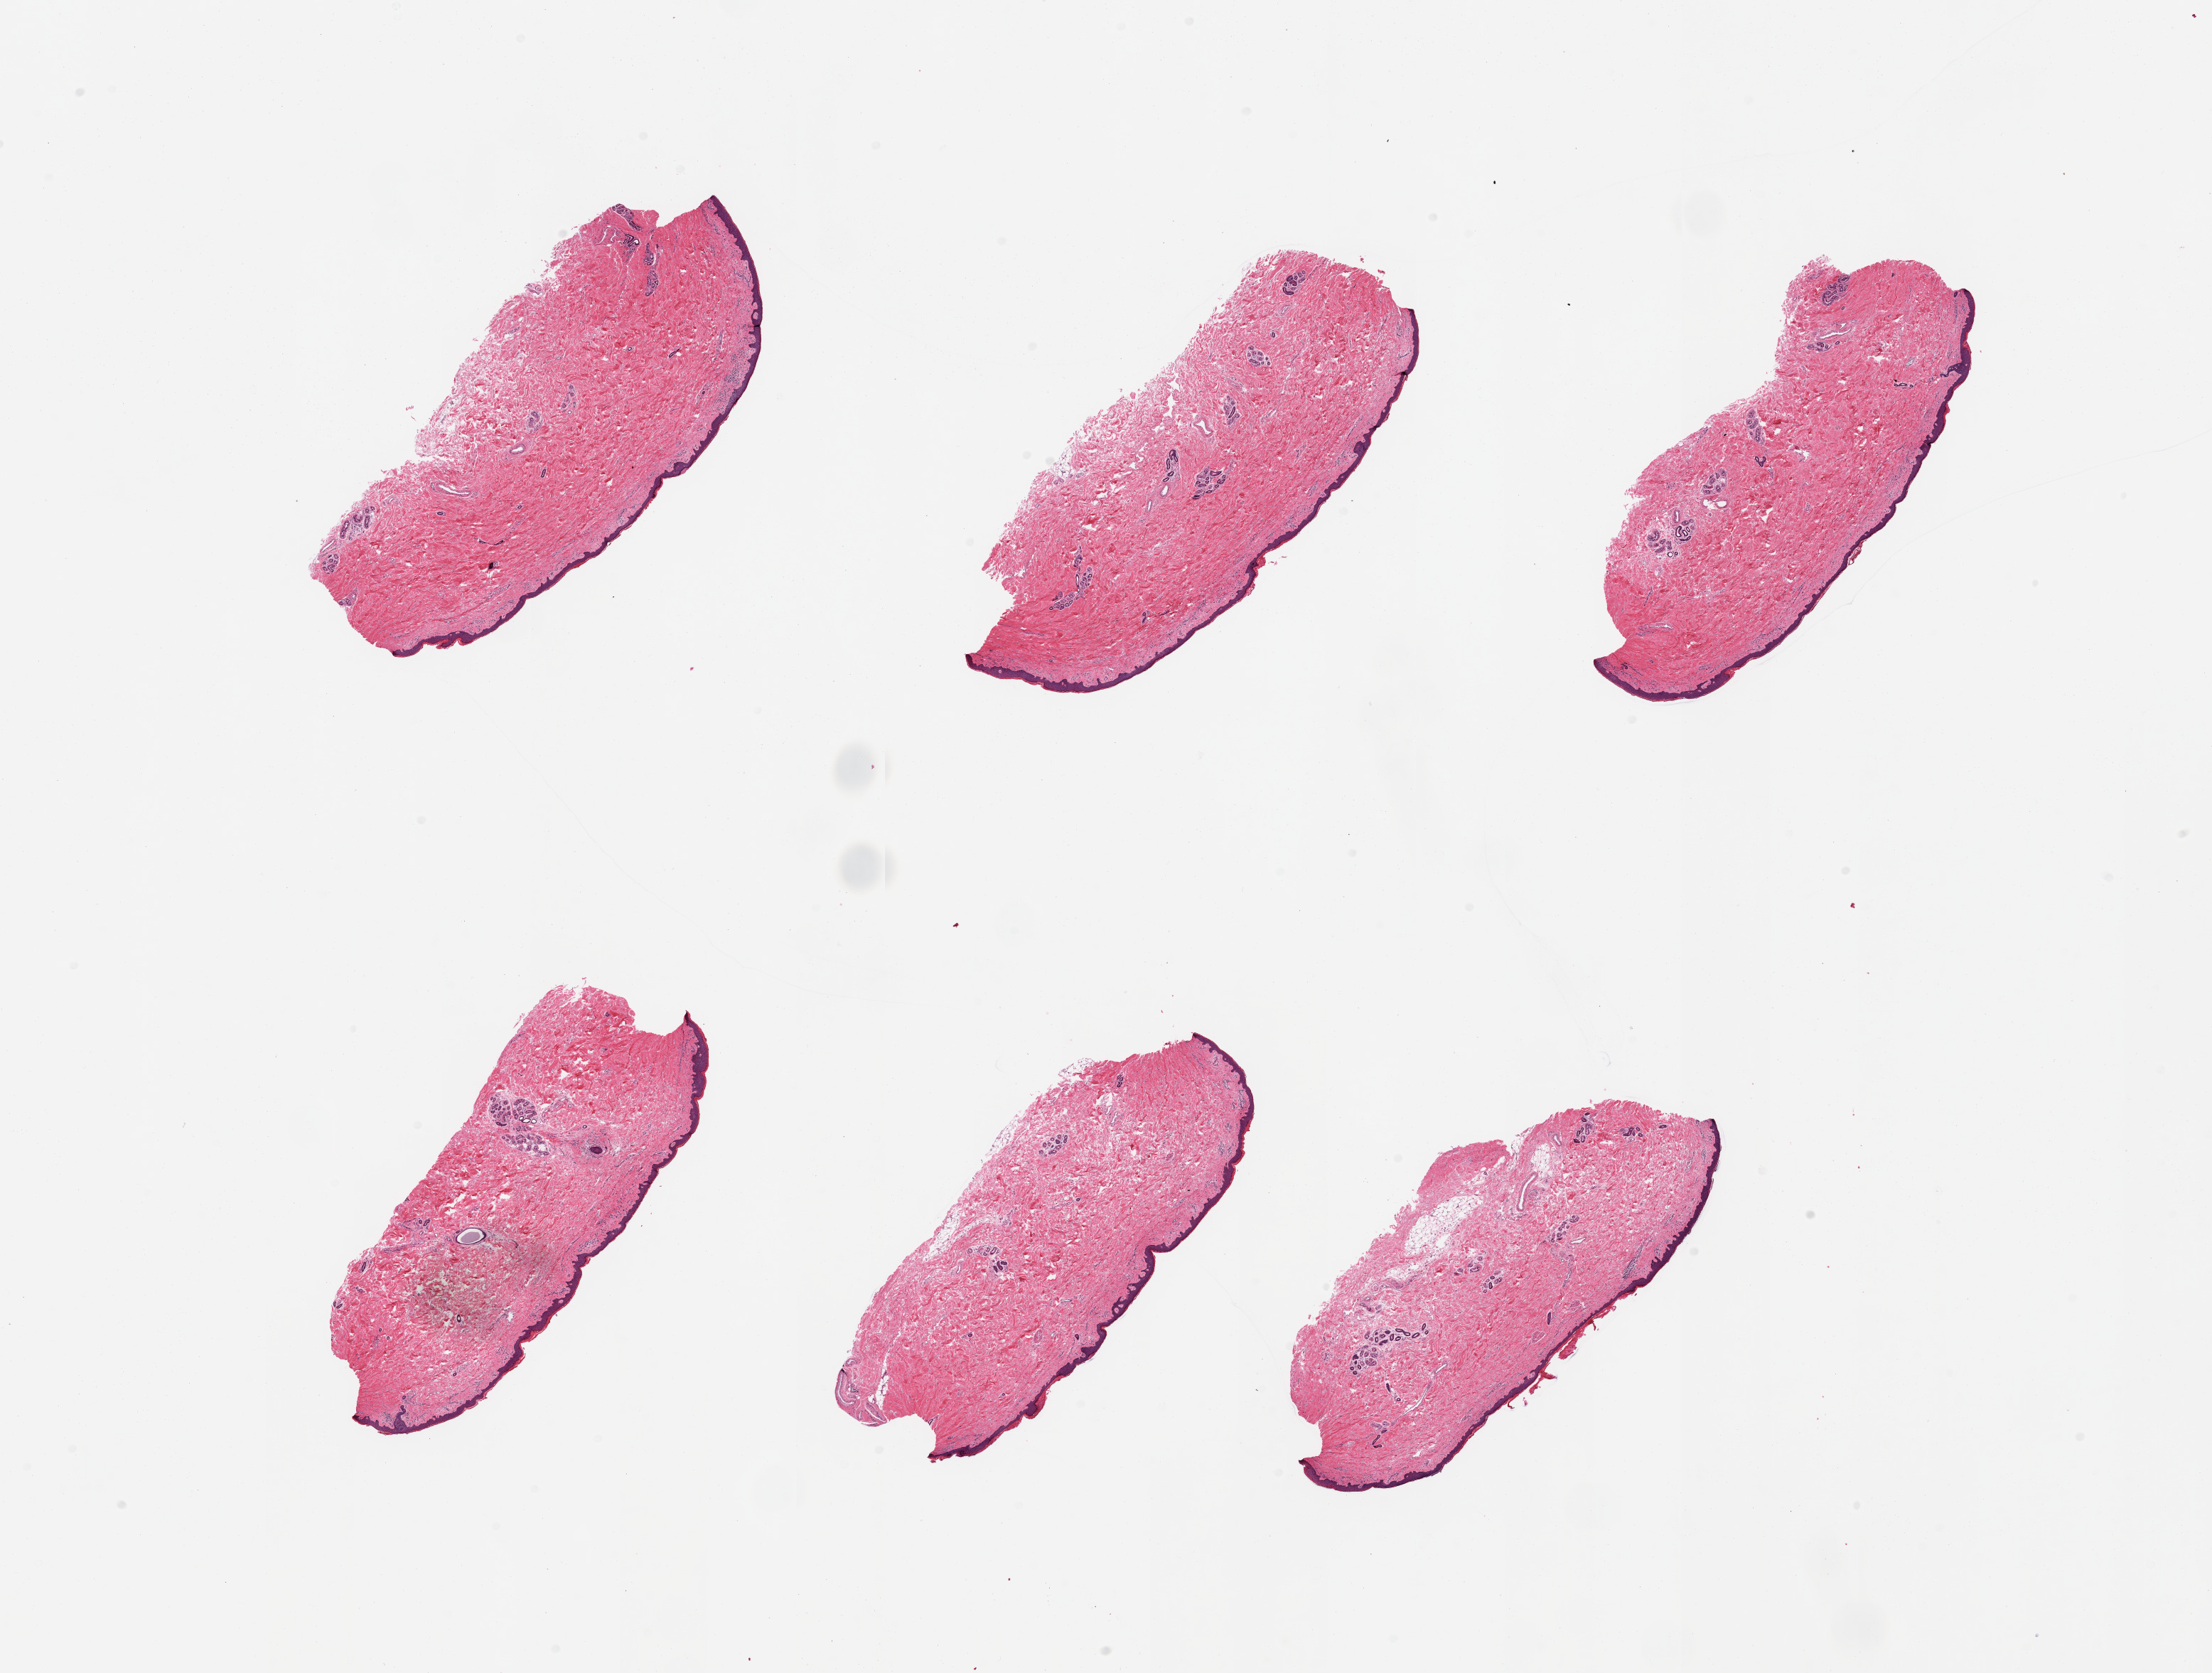
Haematoxylin and eosin whole-slide image, a low-resolution overview of the entire scanned area, about 24.6 x 18.6 mm (acquisition: 20x scan). PAXgene-fixed paraffin-embedded (PFPE) section. Target tissue: skin of suprapubic region. Donor tissue sample. Donor: male.
Pathologist's review note for this sample: 6 pieces; essentially well trimmed skin with focal internal fat; ~45 micron thick epidermis.